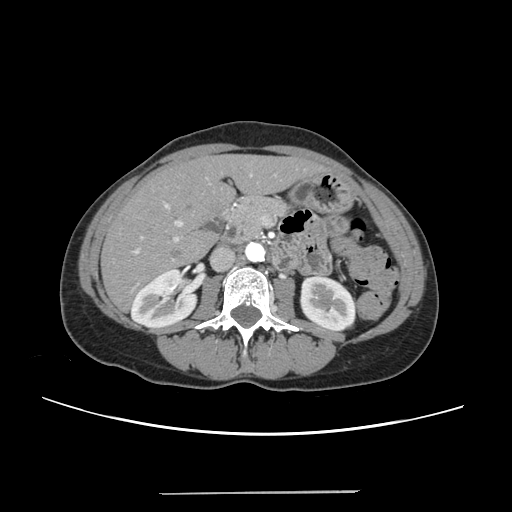
Contrast-enhanced abdominal CT, one axial slice. Slice 108 of 240 in the series (ordered by position). 120 kVp. Intravenous contrast given. Soft-tissue window (W 400 / L 40 HU). 1.25 mm slice thickness. 512 × 512 image matrix, field of view 371 × 371 mm. Female patient, age 60 years. Case-level facts recorded for this patient, not image findings: diagnosis: colorectal cancer liver metastases, imaged before liver resection; multiple liver metastases: no; largest metastasis: 1.5 cm.
Structures marked on this image (expert manual segmentation):
- liver: bounding box [x1, y1, x2, y2] px = [104, 157, 320, 308]
- planned liver remnant (the part of the liver to remain after resection): [104, 157, 320, 308]
- portal vein (with intrahepatic branches): [132, 174, 252, 254]